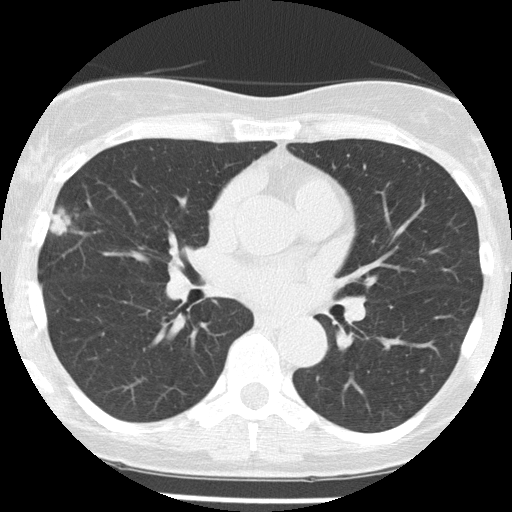
Low-dose screening chest CT, axial slice. First (baseline) screen. Lung window (W 1500 / L -600 HU). 2 mm slice thickness. Slice 72 of 156 in the series. 512 × 512 image matrix, field of view 280 × 280 mm. Female, age 58 years at enrolment. Former smoker at enrolment.
• Expert reader's lesion annotation, bounding box (x1, y1, x2, y2) in pixels: (28, 196, 88, 256).
• The exam's reader record, not a measurement of the box and not confirmed to be the same lesion: non-calcified nodule or mass ≥4 mm, right middle lobe, 18 × 9 mm, spiculated (stellate) margins, soft tissue attenuation.
• Official screen result: positive, change unspecified: nodule(s) >= 4 mm or enlarging nodule(s), mass(es), or other non-specific abnormalities suspicious for lung cancer.